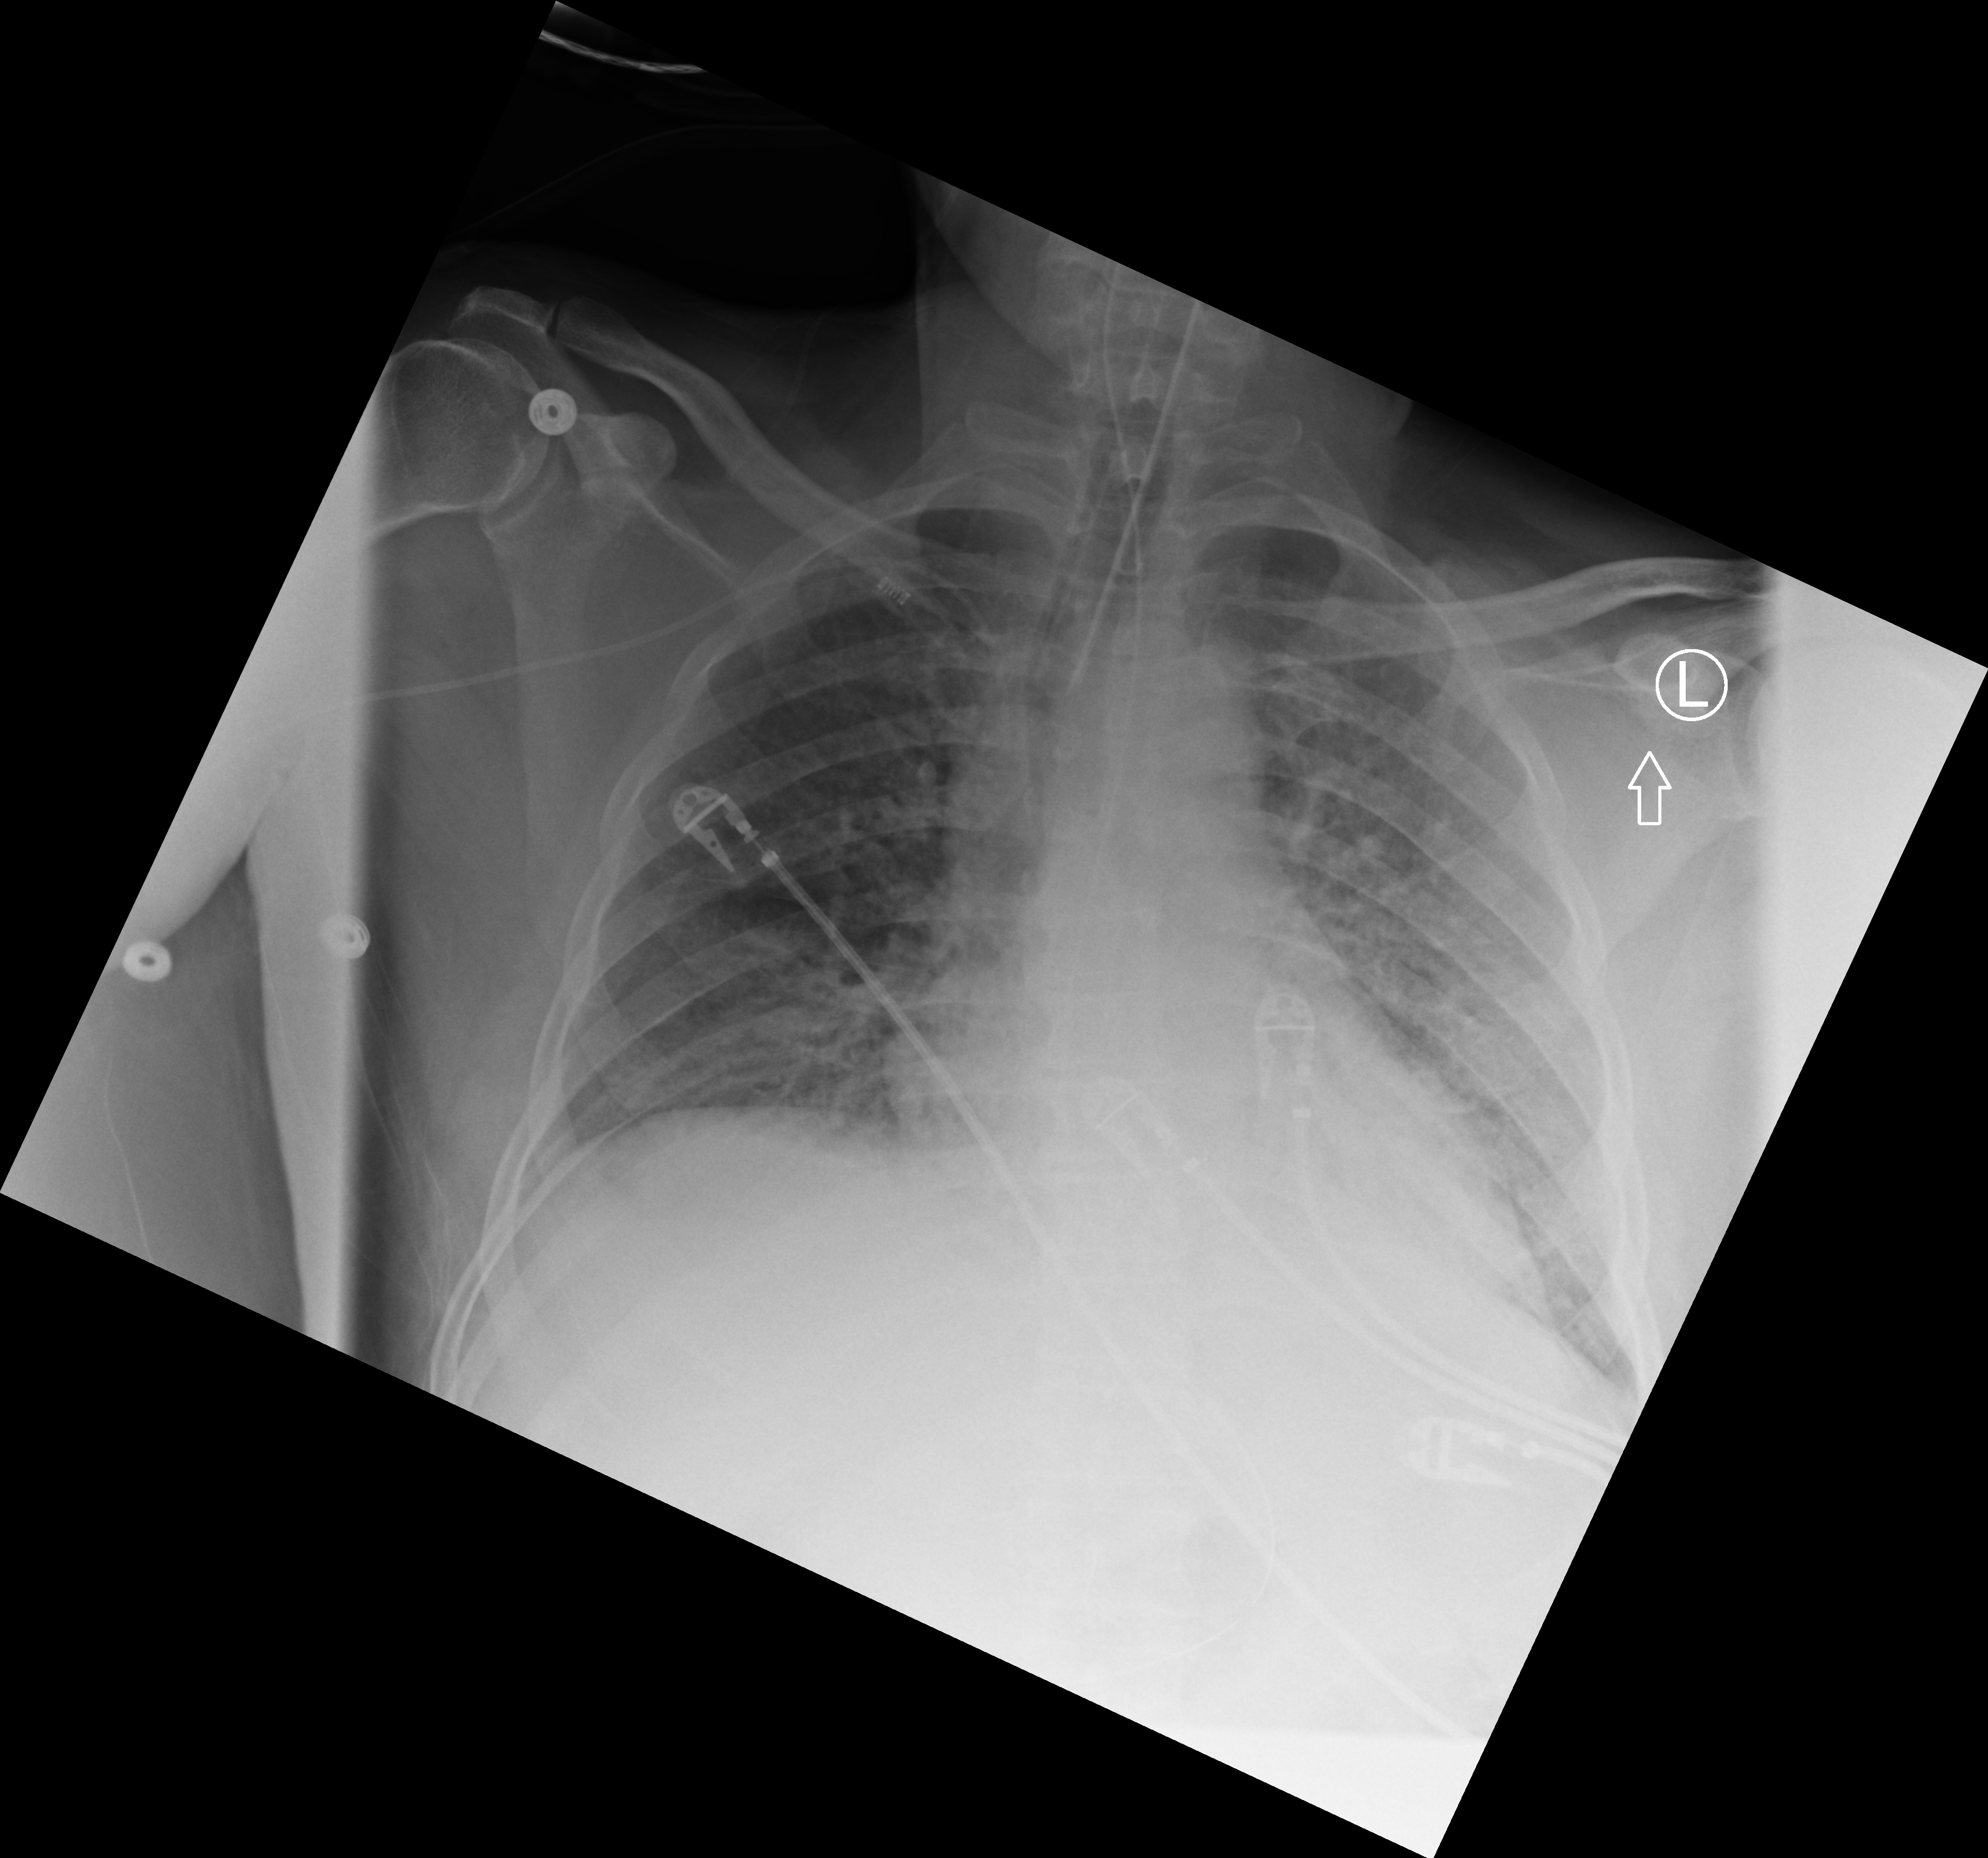
Chest X-ray (portable); anteroposterior (AP) projection. Male patient hospitalised with COVID-19, age 18–59 years.
Hospital-stay facts (about this admission, not read from this image; timing relative to this image not recorded):
- admitted to intensive care during this hospital stay: yes
- hypertension (admission record): yes
- mechanically ventilated during this hospital stay: yes